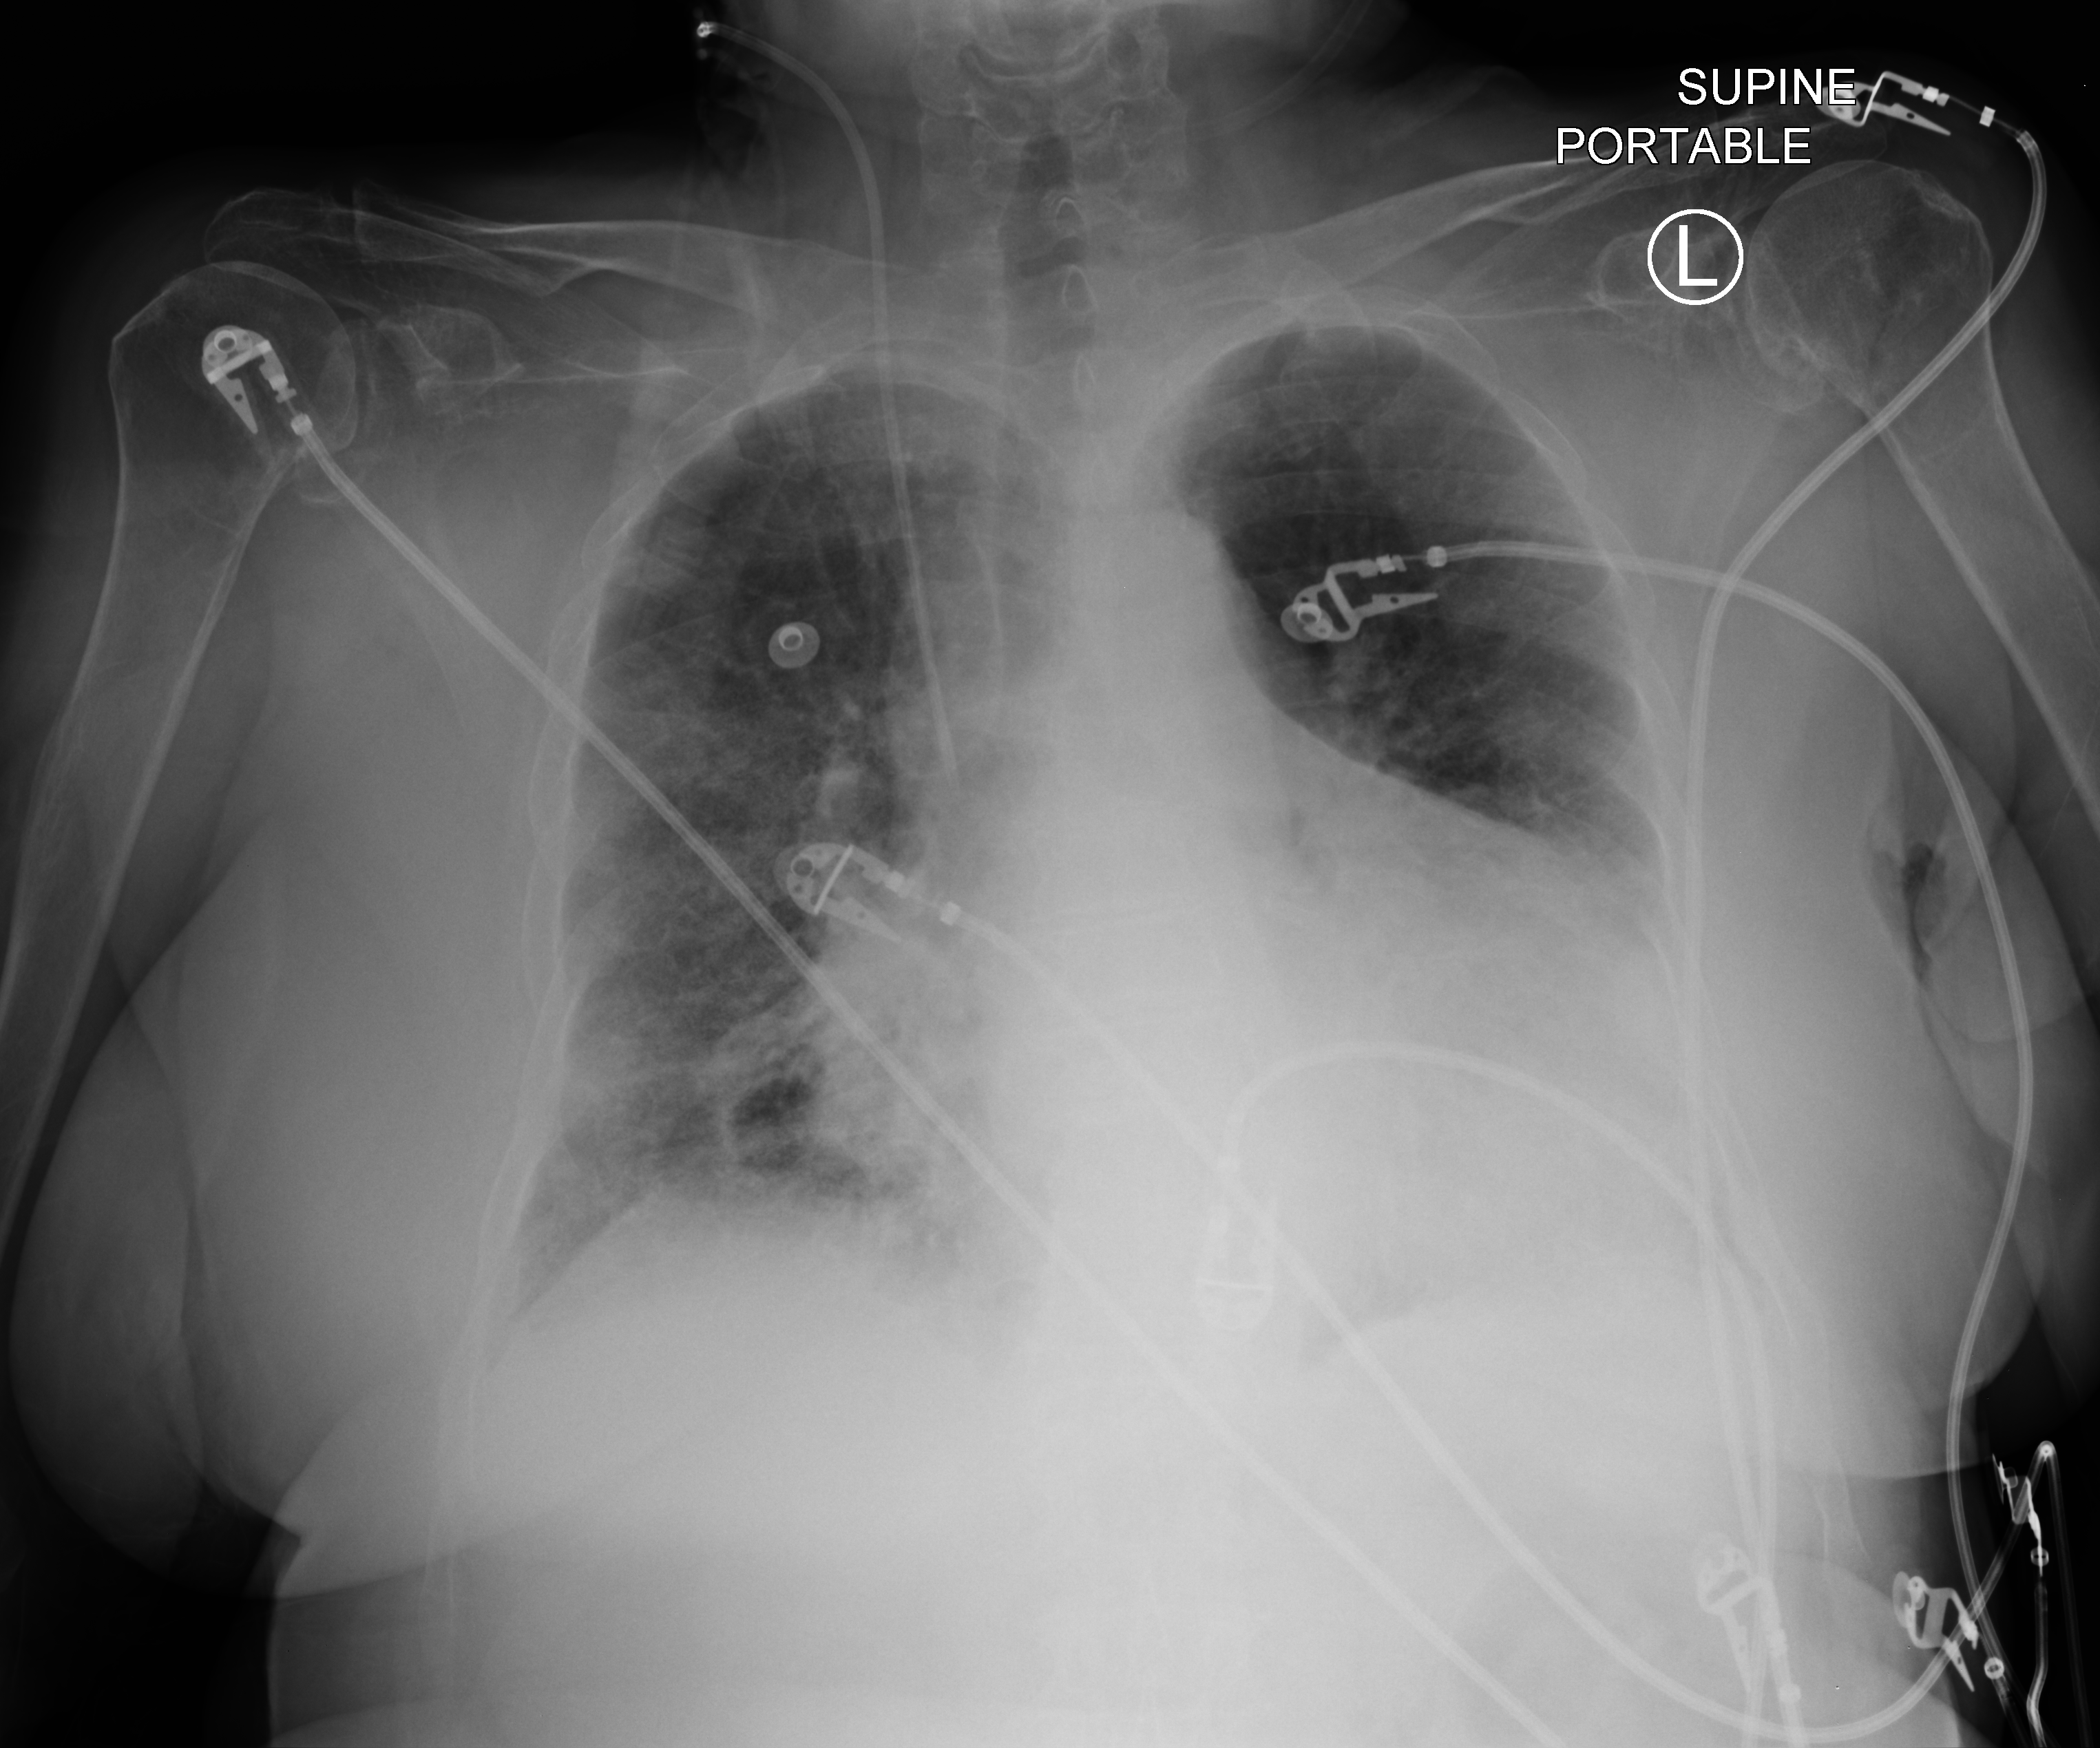
Portable chest radiograph; anteroposterior (AP) projection. Patient hospitalised with COVID-19; female, aged 75–90 years.
Hospital-stay facts (about this admission, not read from this image; timing relative to this image not recorded):
- other chronic lung disease (admission record): no